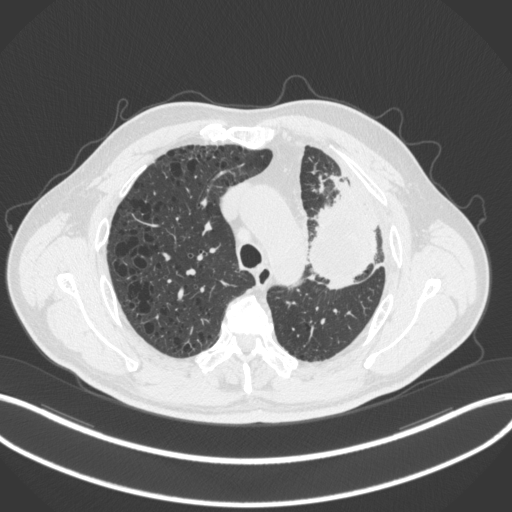
Chest CT, one axial slice. Slice 219 of 286 in the series (ordered by position). 120 kVp. Lung window (W 1500 / L -600 HU). 1 mm slice thickness. 512 × 512 image matrix, field of view 400 × 400 mm. Male patient, age 68 years. From the clinical record (not read from this slice): clinical TNM (as recorded): T3 N3 M1.
Annotated regions visible in this slice (bounding box drawn by a radiologist):
- lung tumour (recorded histology: adenocarcinoma): bounding box <307,168,380,293> (left, top, right, bottom; pixels)